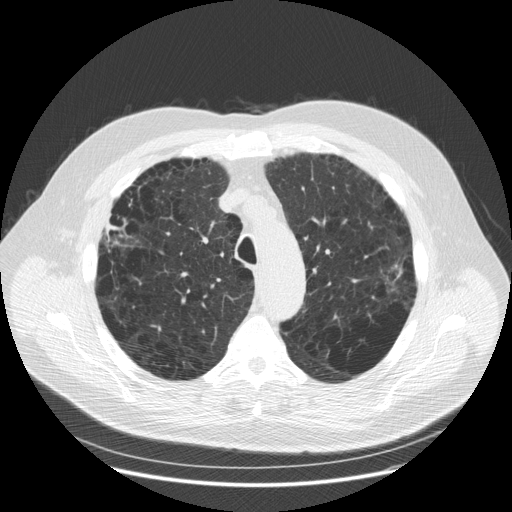
Low-dose screening chest CT, axial slice, baseline annual screen, lung window (W 1500 / L -600 HU), 120 kVp, slice 47 of 179 in the series. Male participant, aged 70 years at enrolment. Current smoker at enrolment.
Expert-annotated lung lesion, bounding box <362,246,421,299> (left, top, right, bottom; pixels). Screening reader's record for this exam (one nodule recorded; not confirmed to be the boxed lesion): non-calcified nodule or mass ≥4 mm, left upper lobe, 25 × 13 mm, spiculated (stellate) margins, soft tissue attenuation. Lung cancer was diagnosed 62 days after this screen: adenocarcinoma, NOS, left upper lobe, moderately differentiated (G2), stage IA (AJCC 6th edition), 22 mm at pathology.